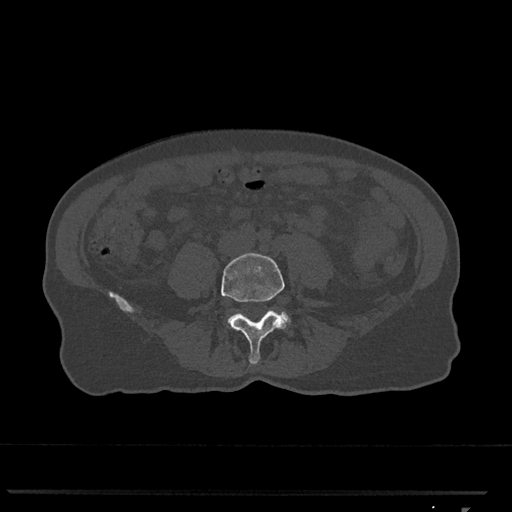
CT including the spine, one axial slice; slice 198 of 793 in the series (ordered by position); reconstruction kernel Br40s/3; 120 kVp; bone window (W 1800 / L 400 HU); 0.5 mm slice thickness; 512 × 512 image matrix, field of view 380 × 380 mm. Female patient, age 62 years. Case-level facts recorded for this patient, not image findings: primary cancer: renal.
Outlined on this slice (semi-automatically segmented with operator editing):
- L4 vertebra: bounding box <221,253,286,365> (left, top, right, bottom; pixels)
- L5 vertebra: <227,311,291,327>